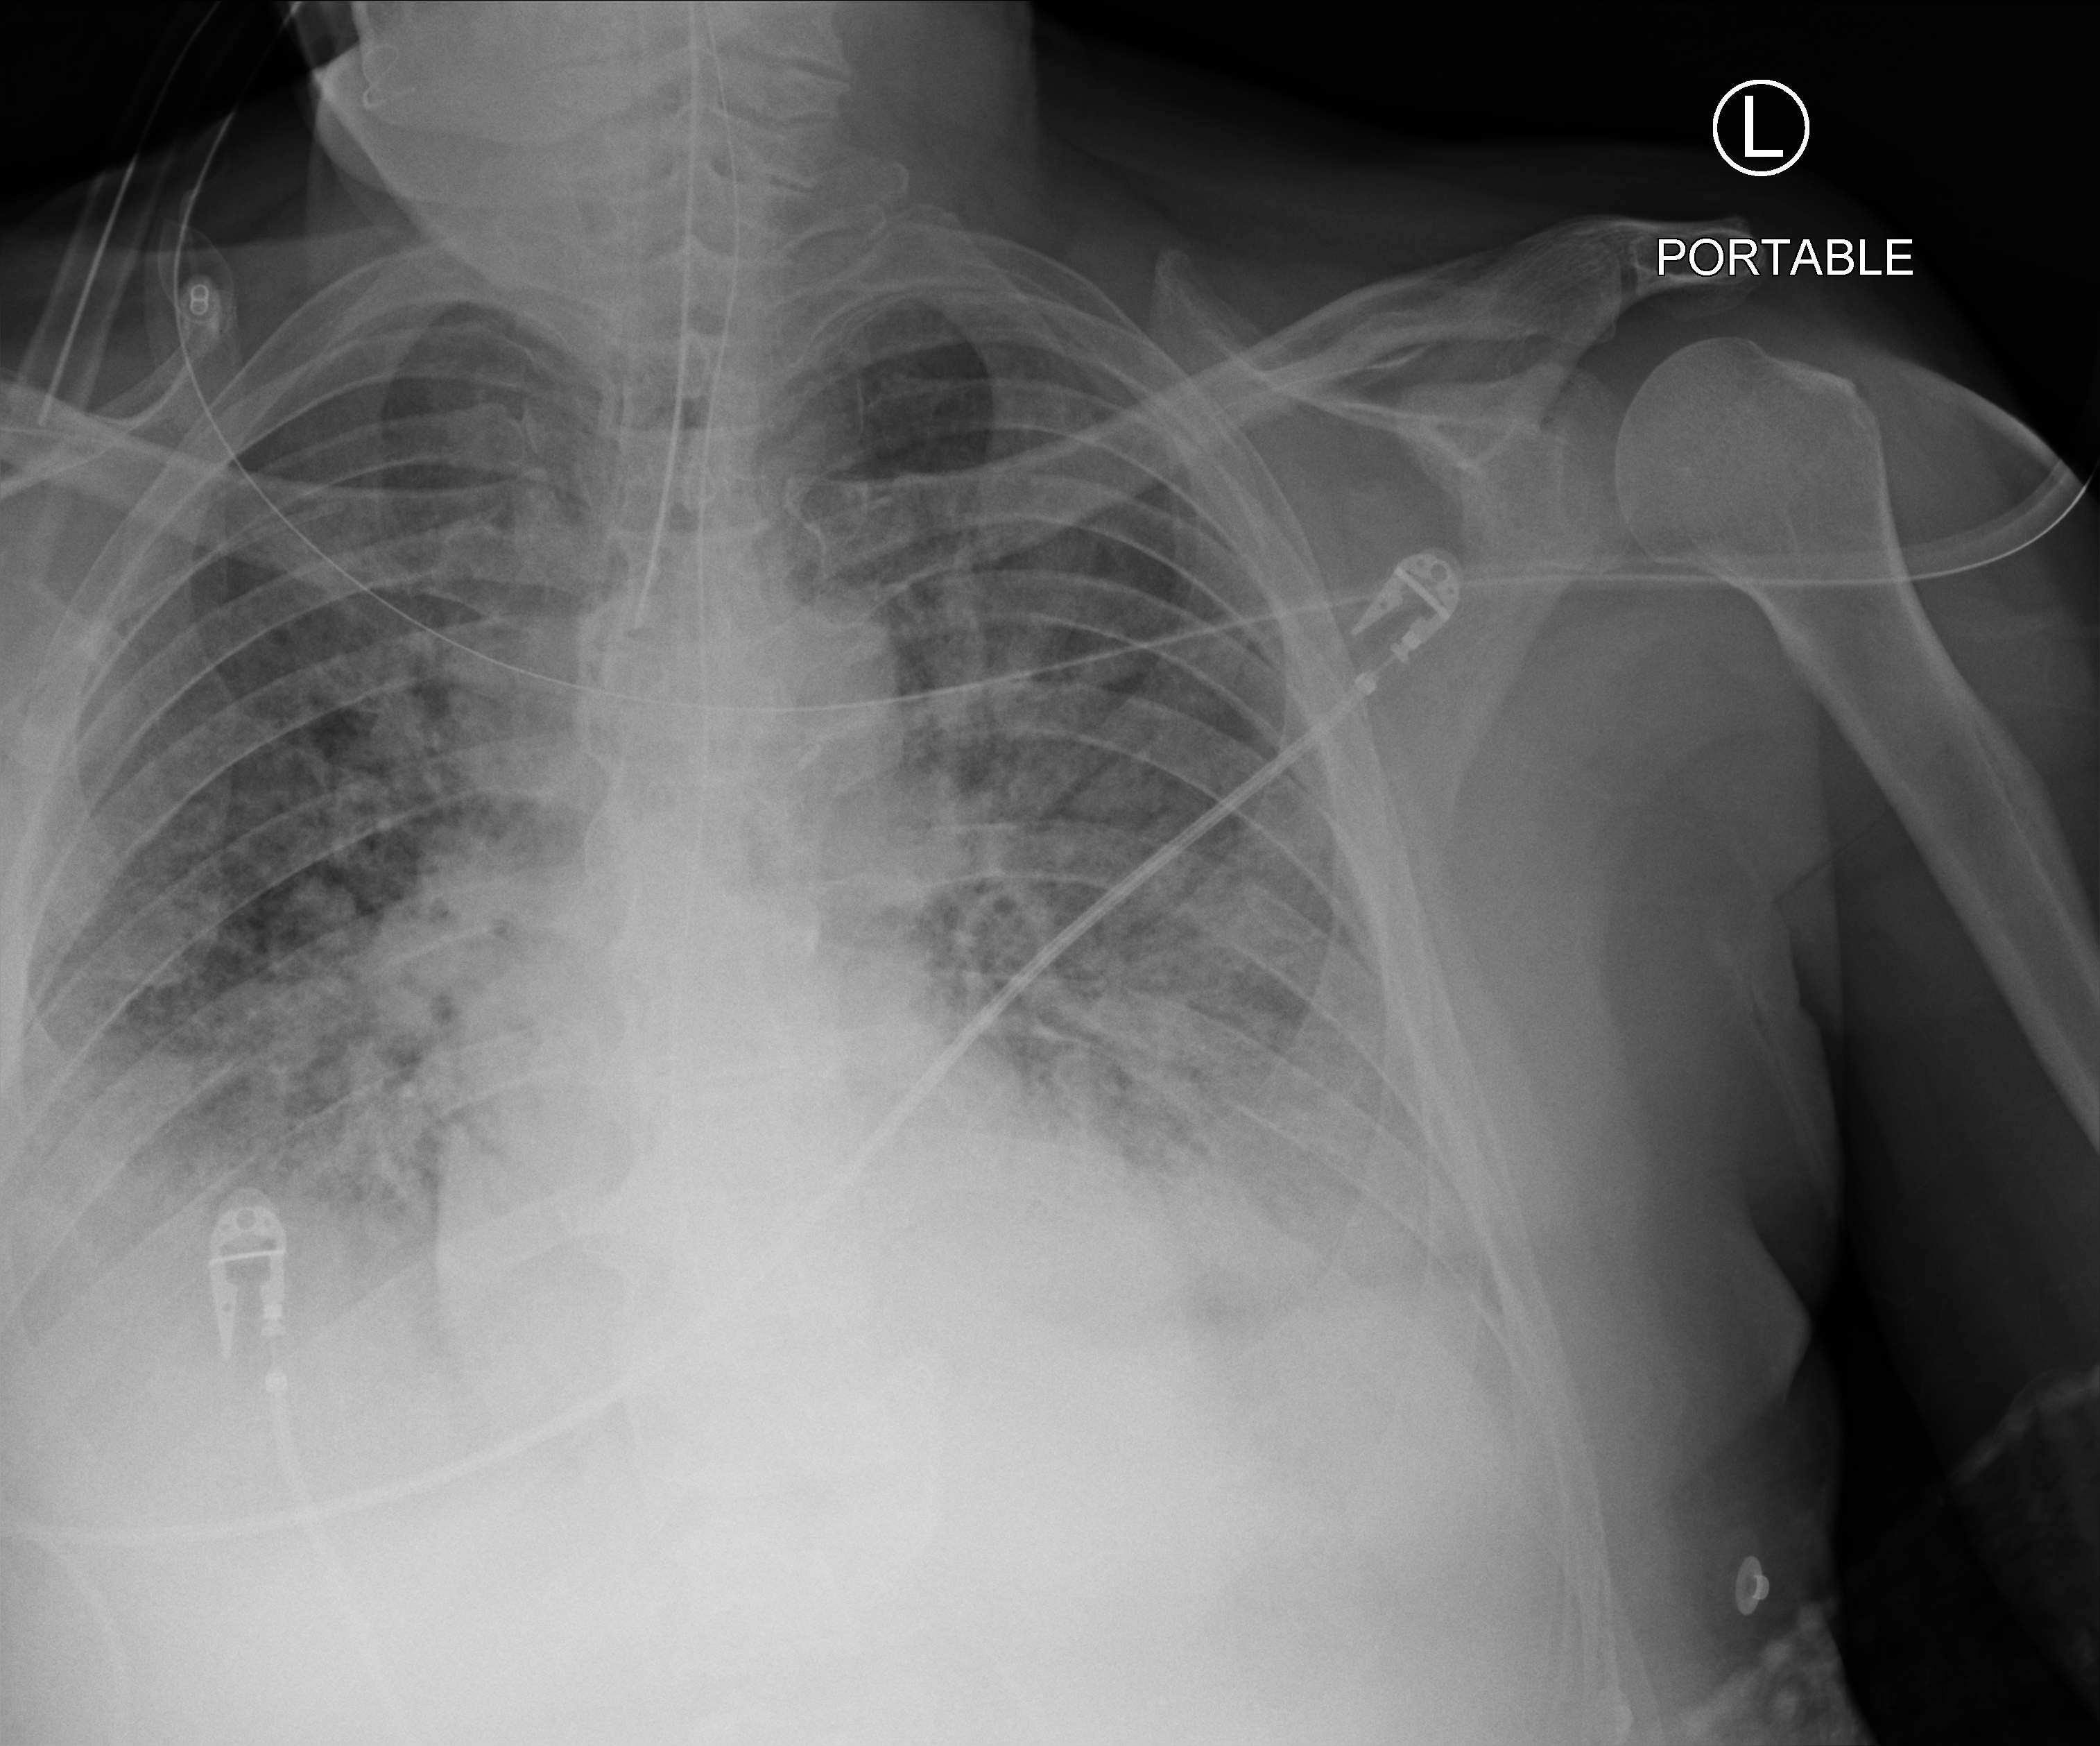
Portable chest radiograph. Patient hospitalised with COVID-19; male, aged 60–74 years.
Hospital-stay facts (about this admission, not read from this image; timing relative to this image not recorded): mechanically ventilated during this hospital stay: yes.